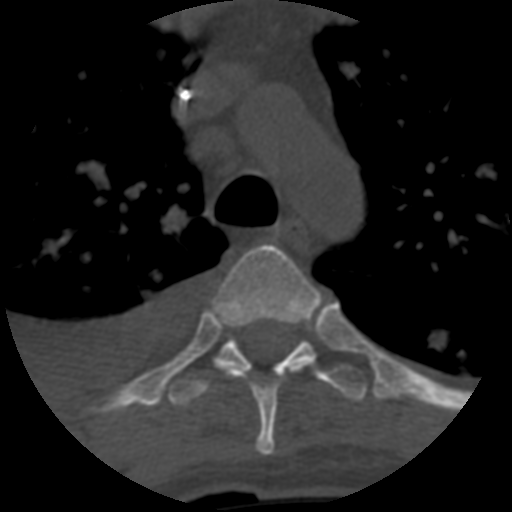
CT including the spine, one axial slice; position 463 of 708 along the scan axis; one of 3 acquisitions stored at this slice position; bone window (W 1800 / L 400 HU); 1.25 mm slice thickness; 512 × 512 image matrix, field of view 160 × 160 mm. Patient age 55 years. Case-level facts recorded for this patient, not image findings: primary cancer: colon.
Structures marked on this image (semi-automatically segmented with operator editing):
- T4 vertebra: bounding box <216,244,316,456> (left, top, right, bottom; pixels)
- T5 vertebra: <168,324,368,407>